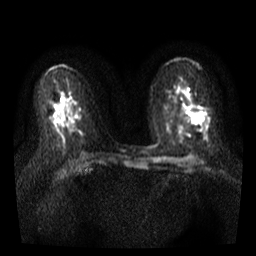
Breast MRI, one axial slice; slice 18 of 35 in the series (ordered by position); diffusion-weighted series; image 2 of 4 stored at this slice position (different b-values; order by instance number); 3 T; 5 mm slice thickness; 256 × 256 image matrix. Female patient.
Annotated regions visible in this slice (expert manual segmentation):
- tumour on diffusion-weighted imaging: bounding box <187,111,204,123> (left, top, right, bottom; pixels)